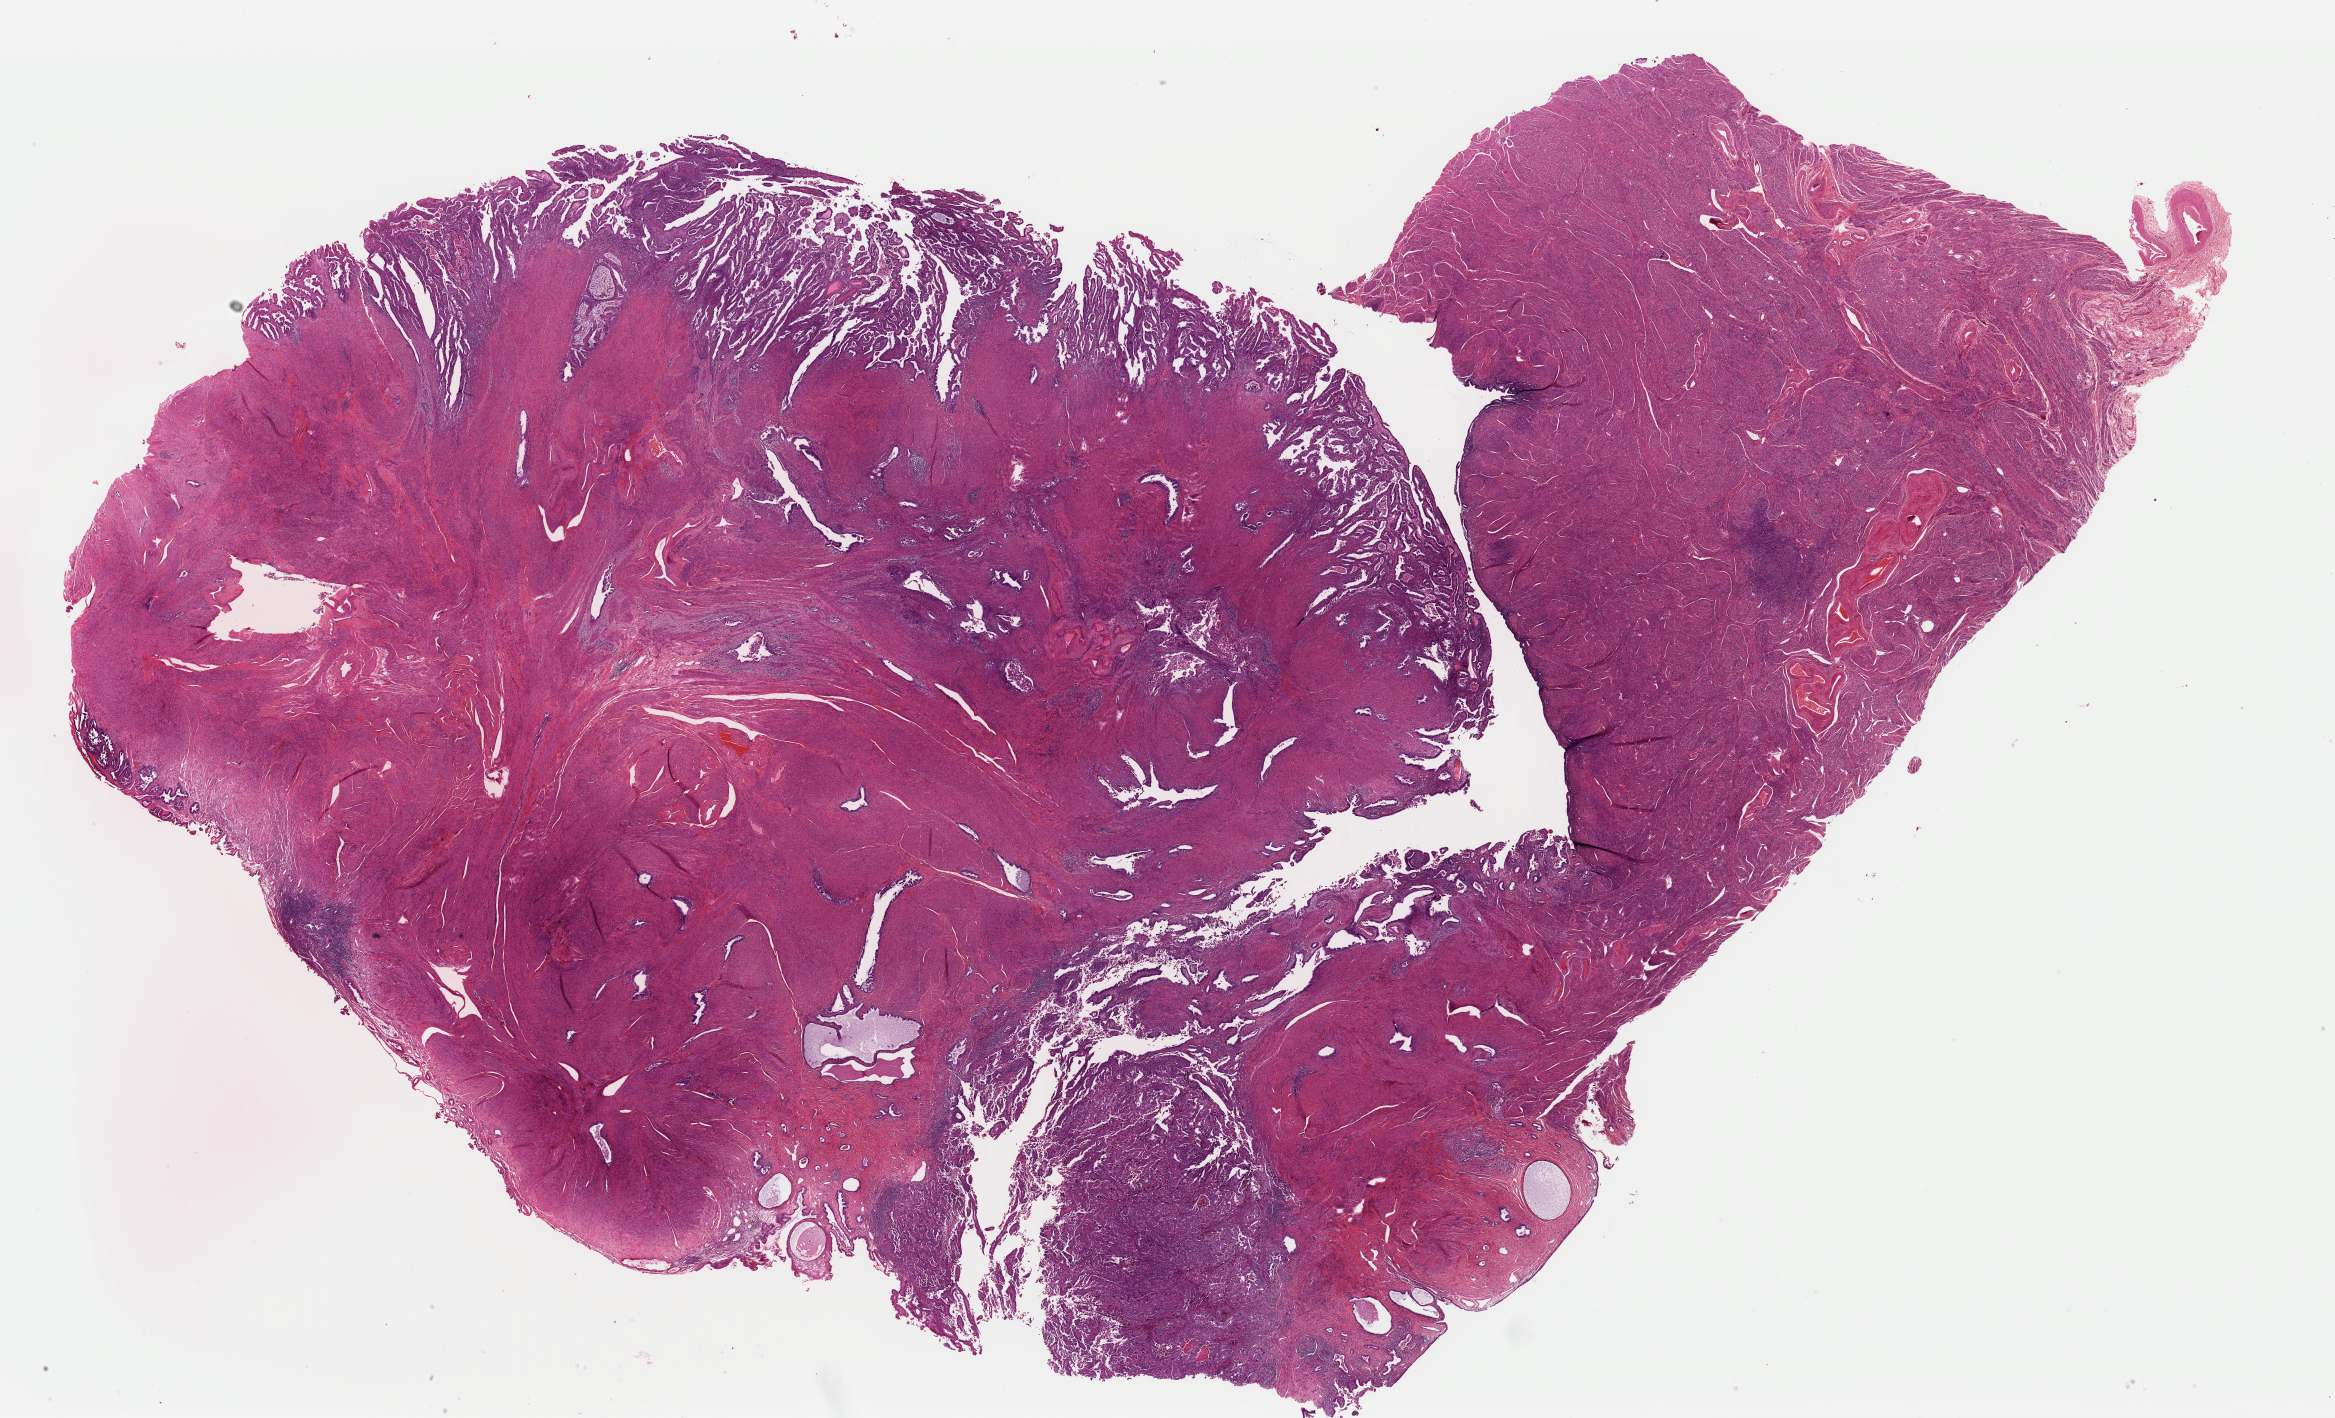
Digitized H&E-stained tissue section (whole slide) — low-resolution overview of the scanned area, about 36.9 x 22.4 mm, formalin-fixed paraffin-embedded (FFPE) diagnostic section, sample: primary tumour, uterus. Patient: female, age at initial diagnosis 77 years. Histologic grade: G3 (poorly differentiated).
Histologic diagnosis: Serous cystadenocarcinoma, NOS (endometrium). FIGO stage: IA.